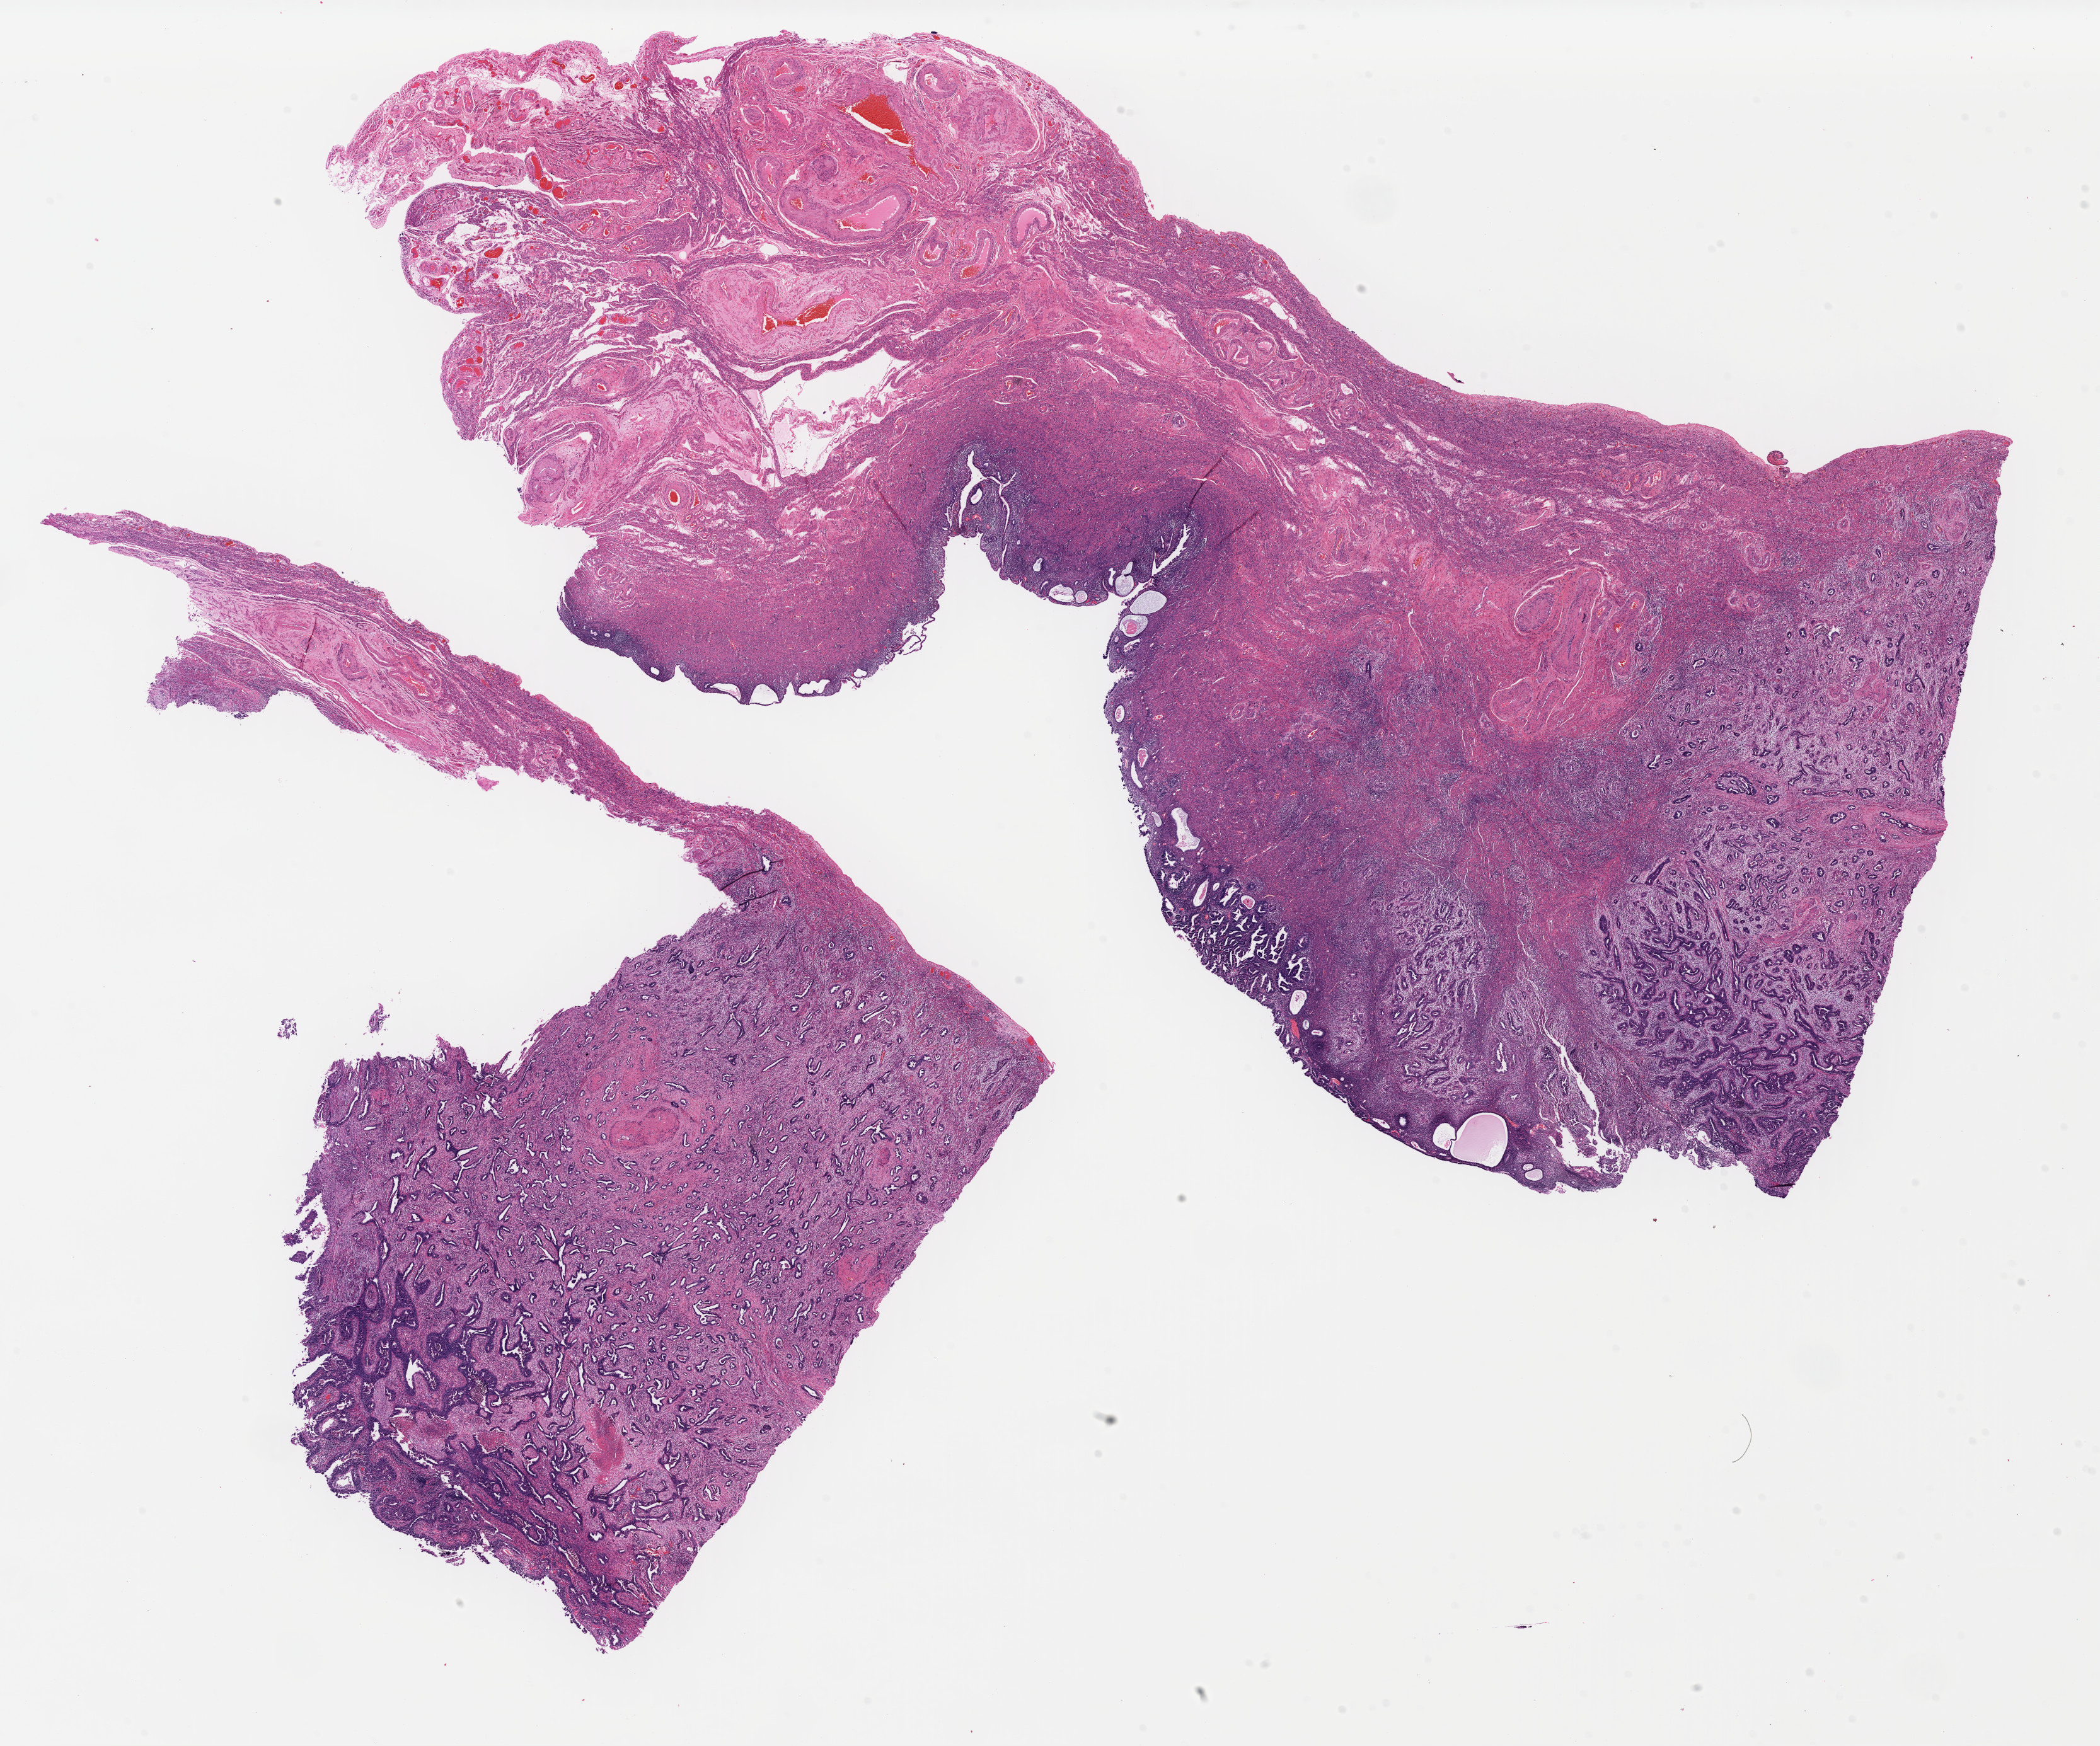
H&E-stained whole-slide image, shown as a low-resolution overview of the whole scanned area (about 26.2 x 21.8 mm, from a 40x scan); FFPE section; sample: primary tumour, uterus. Female patient; age at initial diagnosis 79 years. Histologic grade: G3 (poorly differentiated).
Pathologic diagnosis: Serous cystadenocarcinoma, NOS (endometrium). FIGO stage: IVB.